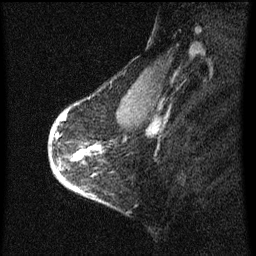
Breast MRI (dynamic contrast-enhanced), one sagittal slice. Slice 48 of 60 in the series (ordered by position). Dynamic contrast-enhanced series, image 2 of 3 at this slice position (ordered by acquisition). 1.5 T. TE 4.2 ms, TR 8 ms. 2 mm slice thickness. 256 × 256 image matrix, field of view 180 × 180 mm. Patient: female, 56 years.
Outlined on this slice (semi-automatically segmented with operator editing):
- analysis volume of interest (the breast-tissue region the enhancement analysis was run in; not a lesion): bounding box (x1, y1, x2, y2) in pixels: (52, 110, 103, 193)
- tumour enhancement mask (voxels above the 70 % enhancement threshold inside the analysis volume of interest): (60, 114, 99, 191)